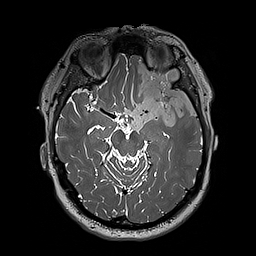
Brain MRI from a brain-tumour surgery series, one axial slice. Position 129 of 192 along the scan axis. 256 × 256 image matrix, field of view 250 × 250 mm. From the clinical record (not read from this slice): histopathology: Oligodendroglioma; WHO grade: 3; IDH mutation: yes; tumour location: Left Sylvian Fissure (Temporal).
Structures marked on this image (manually delineated by an expert):
- tumour: bounding box <124,61,197,132> (left, top, right, bottom; pixels)